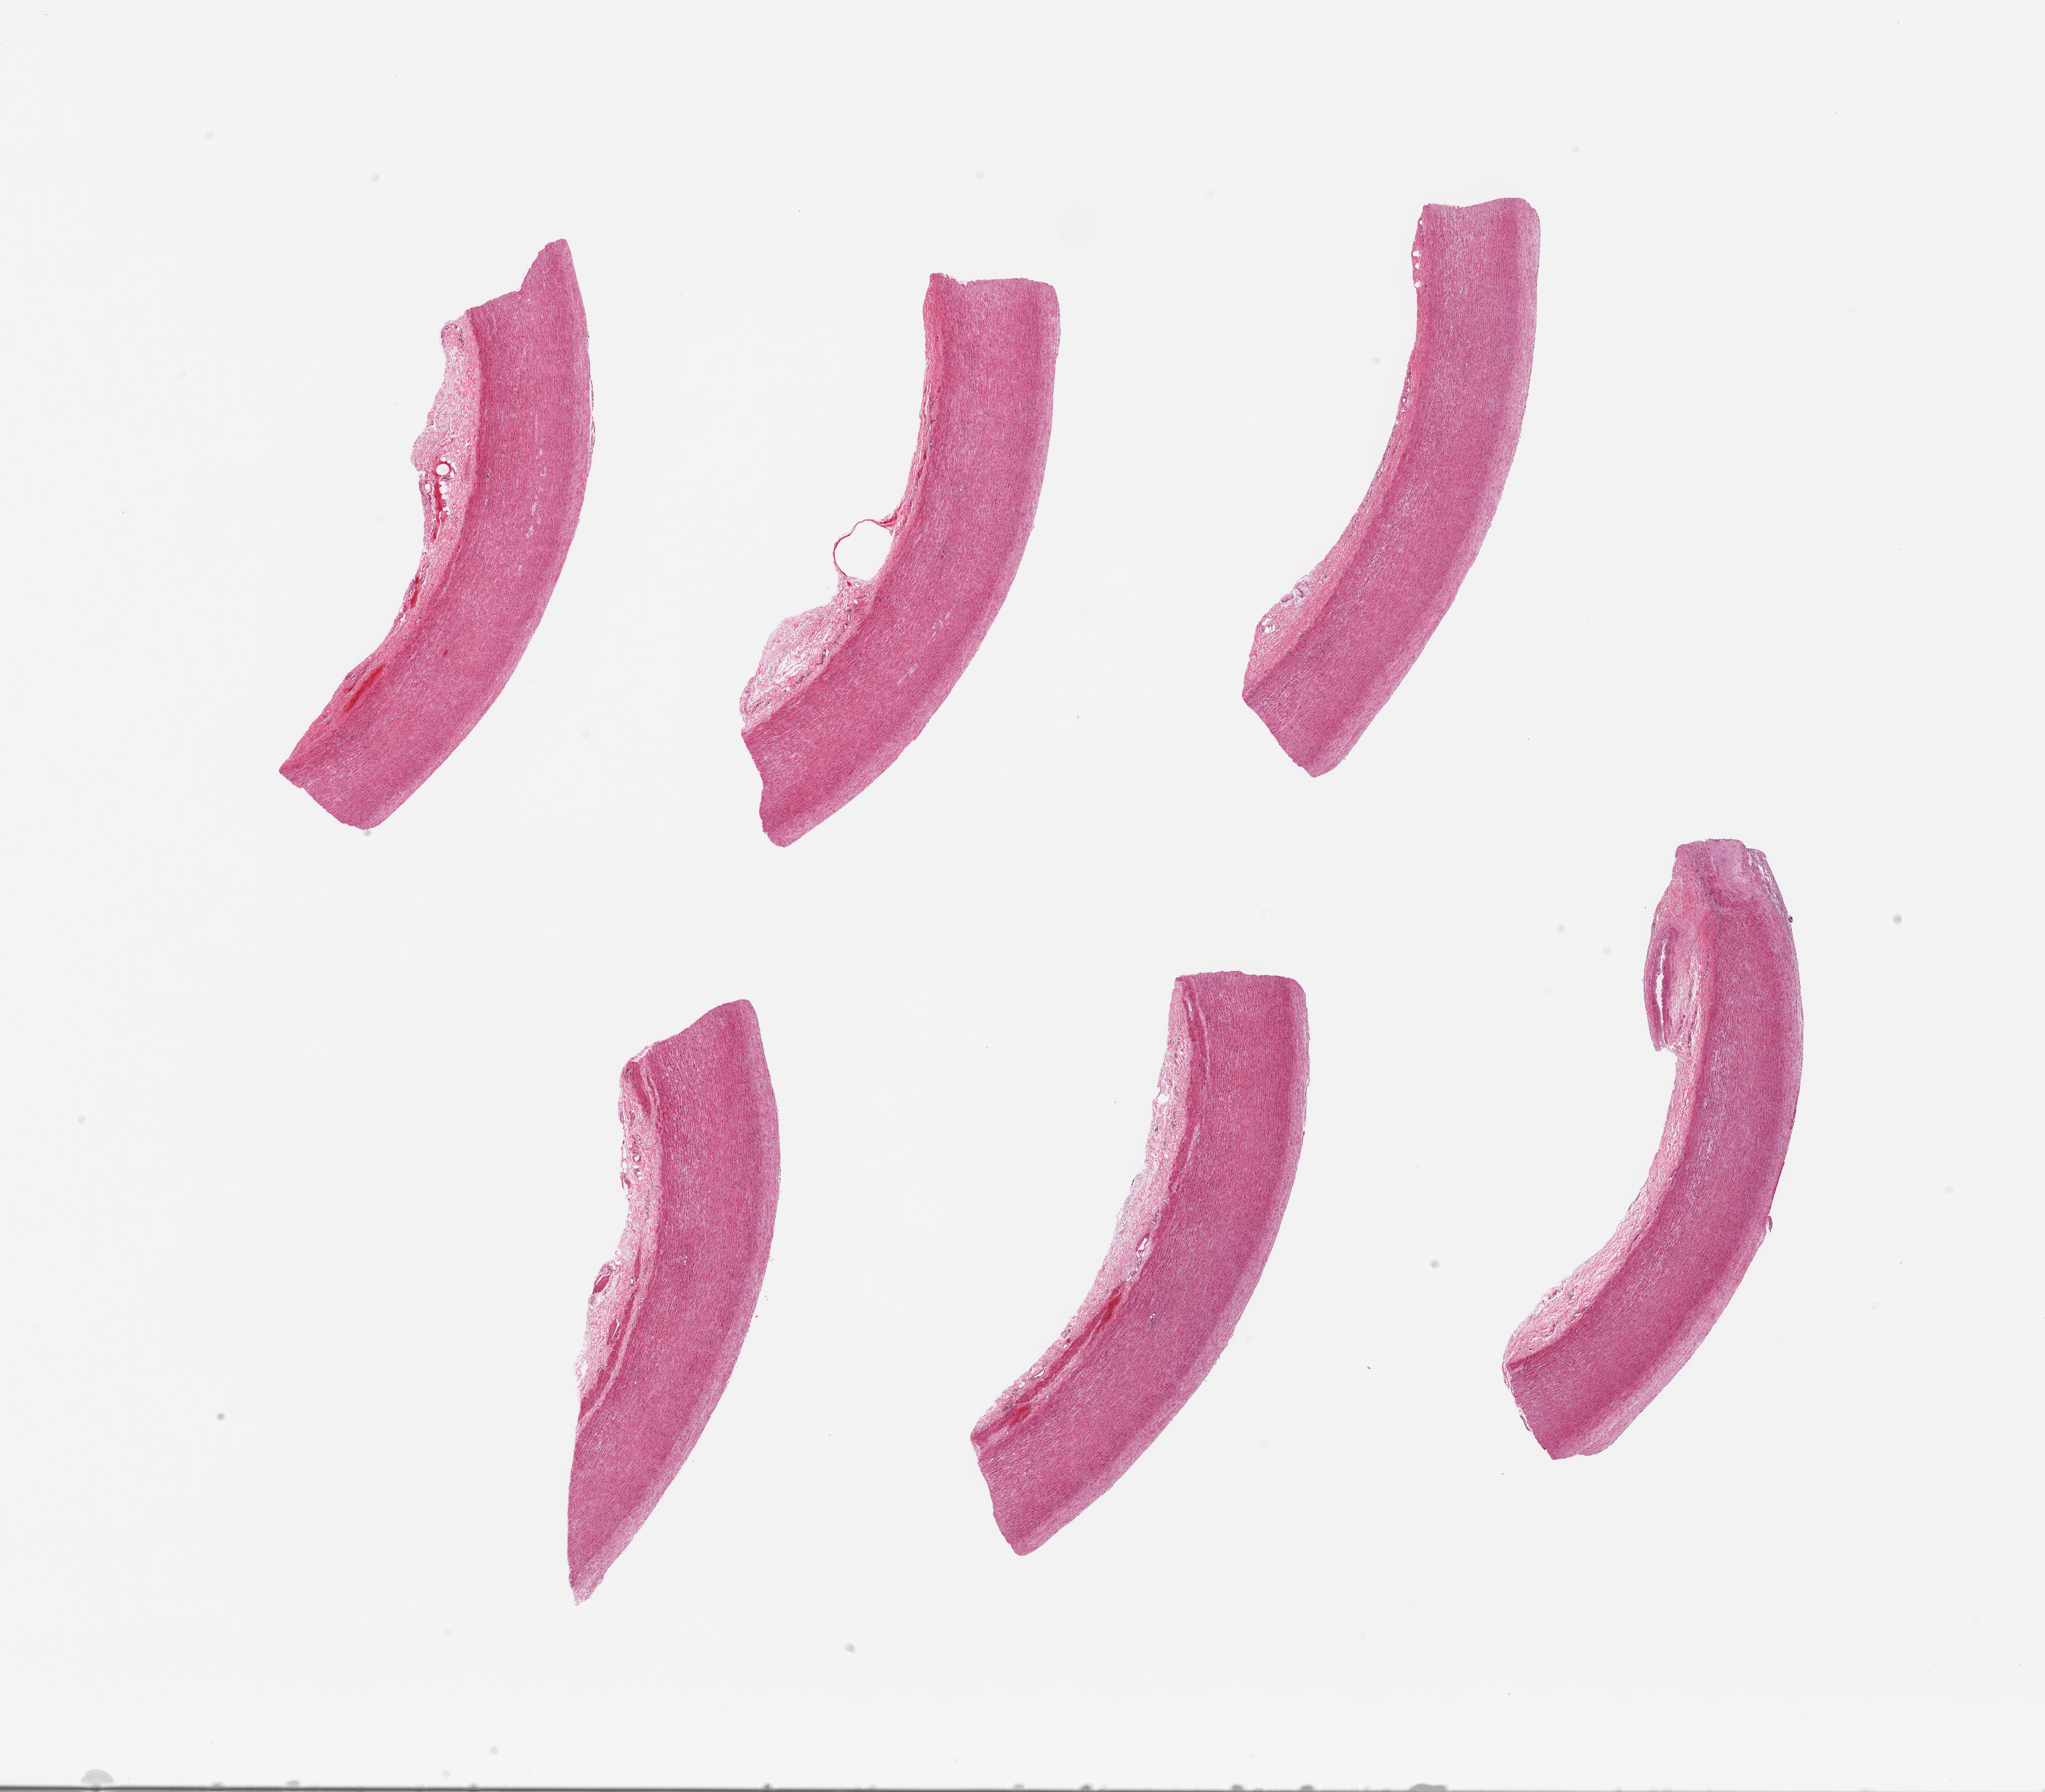
H&E whole-slide image, shown as a low-resolution overview of the whole scanned area (about 23.6 x 20.7 mm); PAXgene-fixed paraffin-embedded (PFPE) section; section of aorta (target tissue); tissue donor sample. Donor sex: male.
Review note (as recorded): 6 pieces; atherosis.